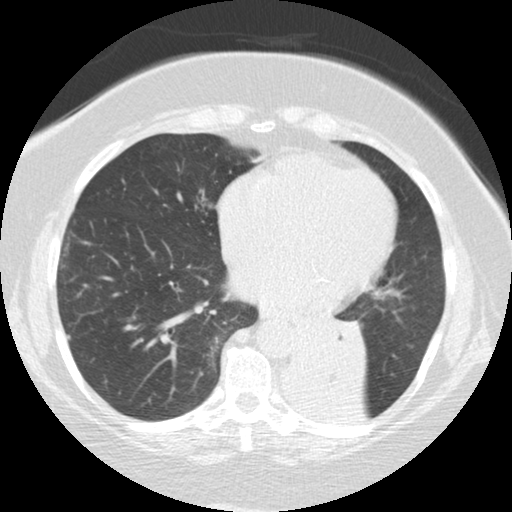
Chest CT (low-dose screening protocol), one axial image, baseline screening round, lung window (W 1500 / L -600 HU), 2.5 mm slice thickness, standard (soft-tissue) reconstruction kernel (STANDARD), slice 80 of 136 in the series, 512 × 512 image matrix. Female participant, aged 71 years at enrolment. Former smoker at enrolment.
Lesion marked by an expert reader, bounding box [x1, y1, x2, y2] px = [279, 302, 370, 384]. Screening reader's record for this exam (one nodule recorded; not confirmed to be the boxed lesion): non-calcified nodule or mass ≥4 mm, right middle lobe, 5 × 5 mm, smooth margins, soft tissue attenuation. Note: the box lies in the patient's left hemithorax on this image, whereas the reader's record names the right lung; they may be different findings. Official screen result: positive, change unspecified: nodule(s) >= 4 mm or enlarging nodule(s), mass(es), or other non-specific abnormalities suspicious for lung cancer. Later outcome: lung cancer diagnosed 46 days after this screen — large cell carcinoma, NOS, left lower lobe, mediastinum, other location, poorly differentiated (G3), stage IV (AJCC 6th edition), 50 mm at pathology.